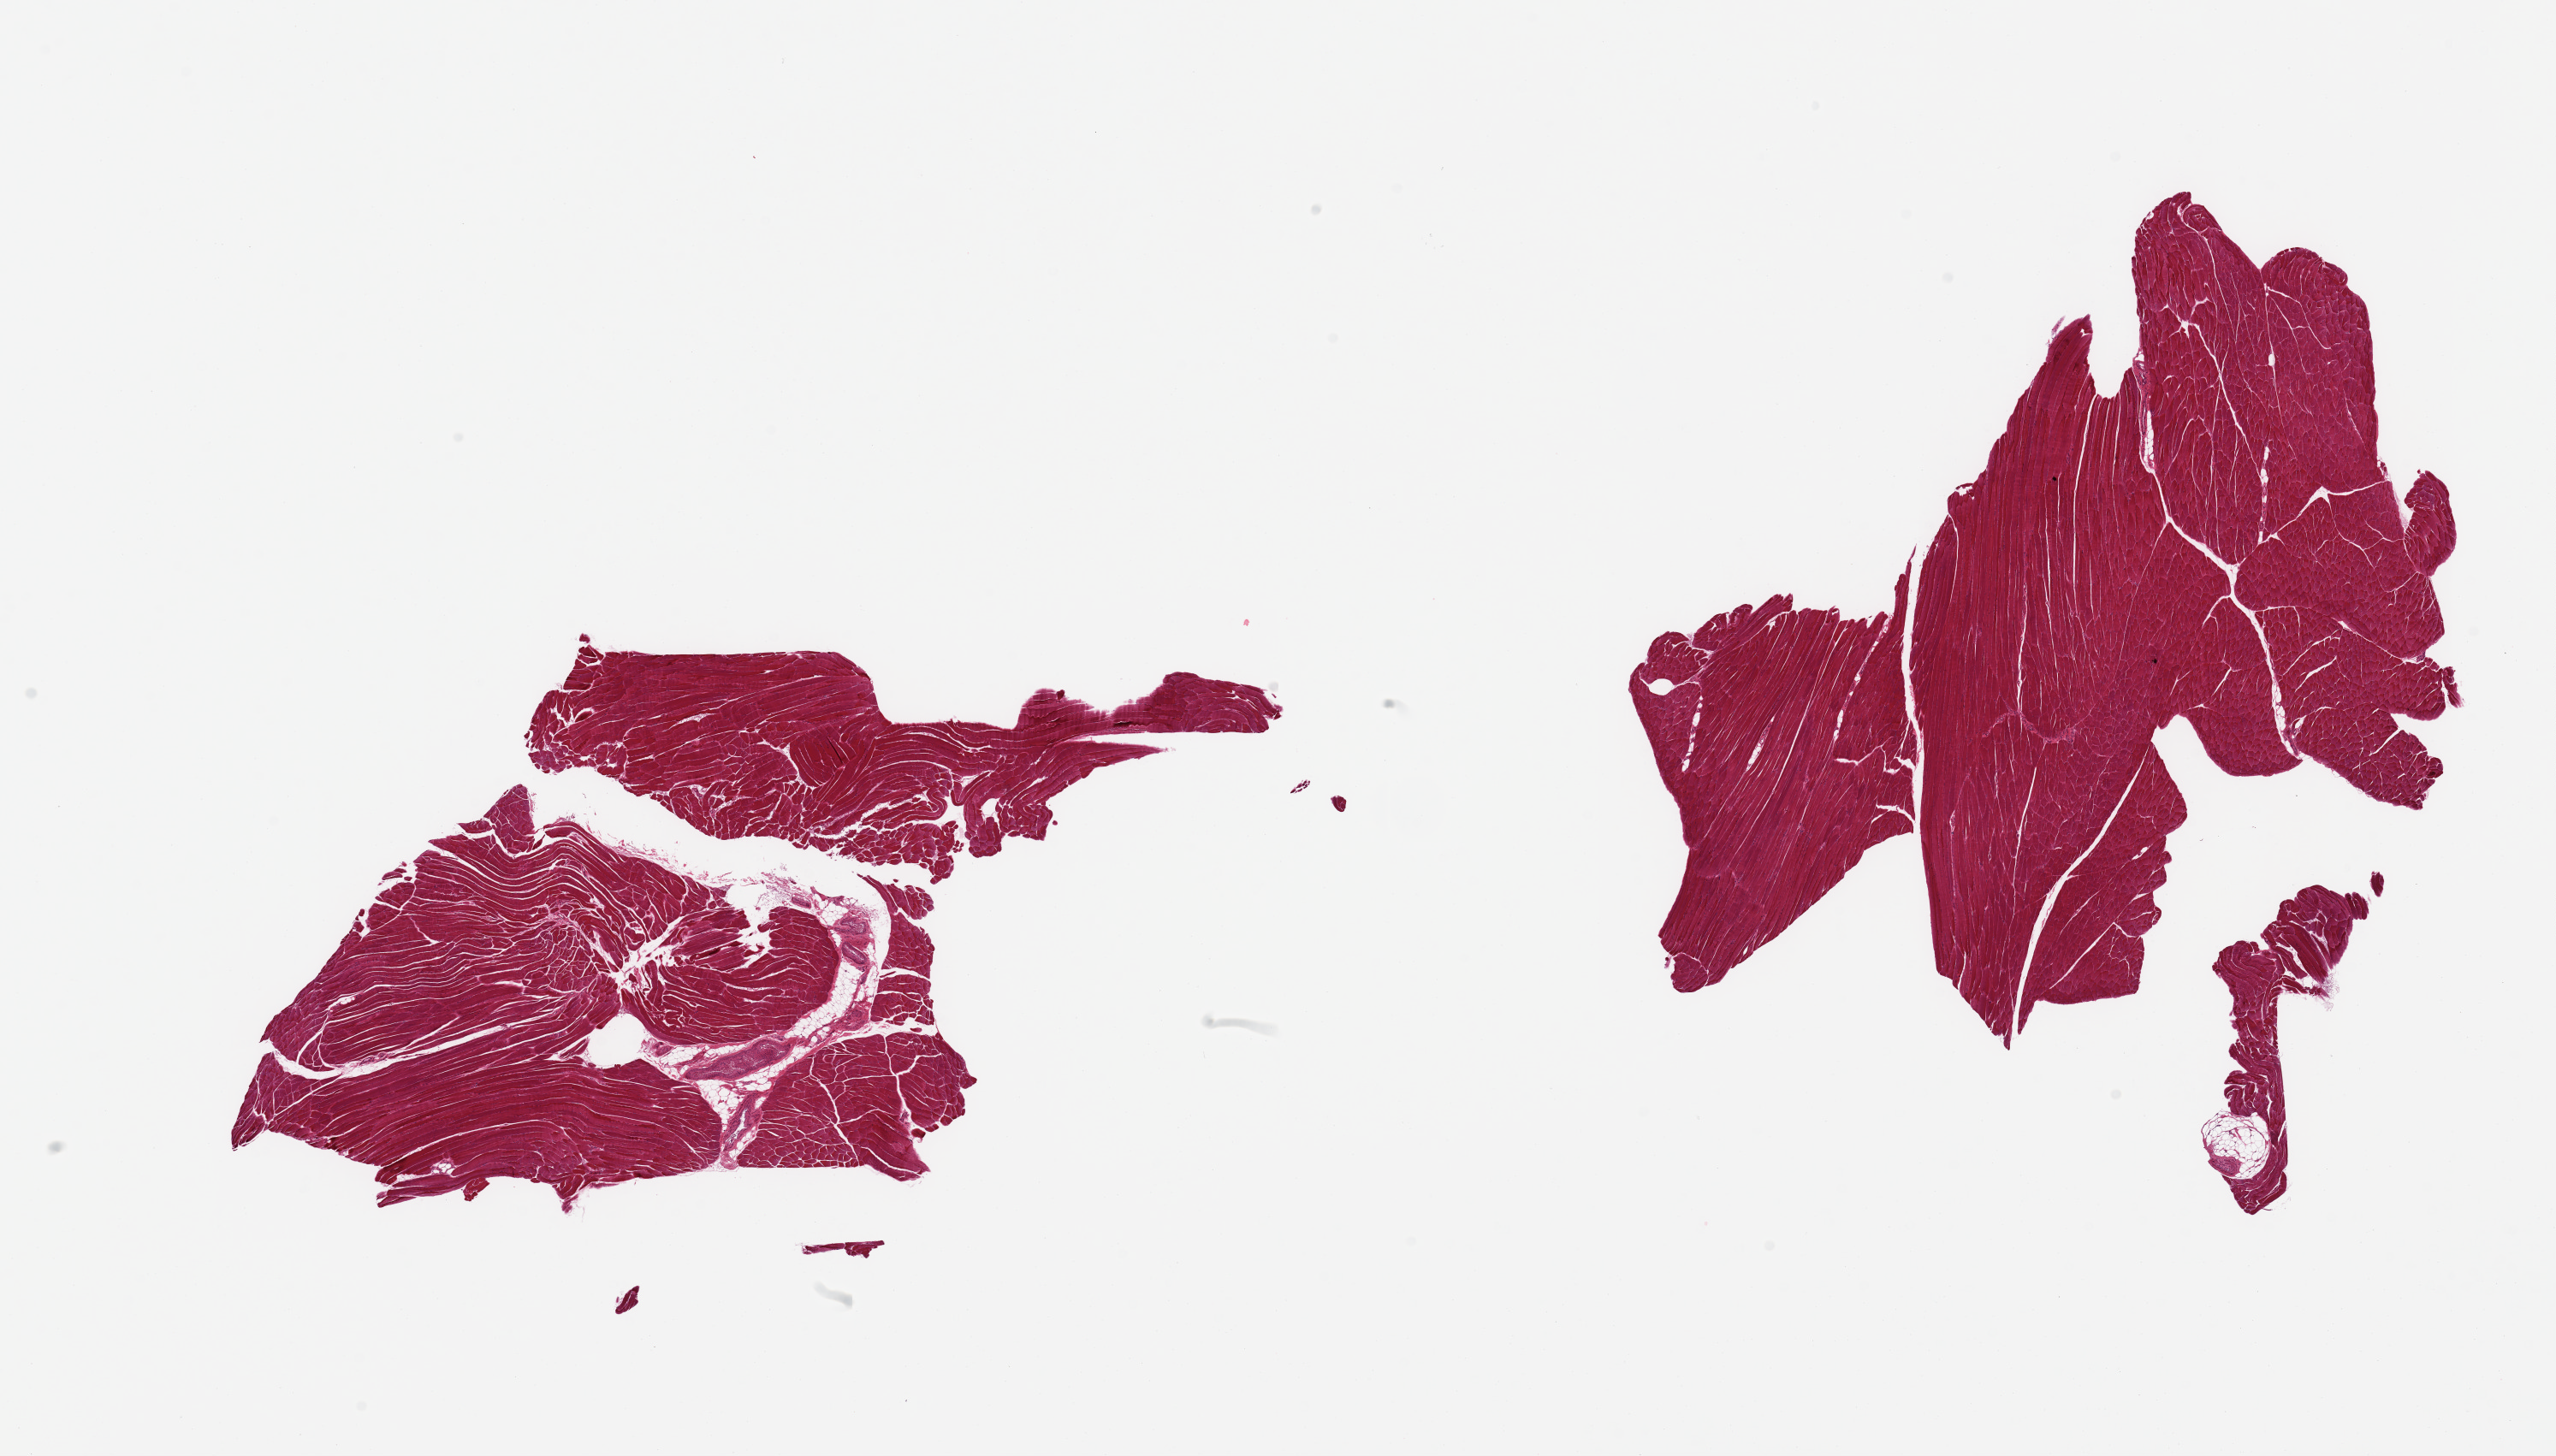
Hematoxylin and eosin (H&E) whole-slide image — whole scanned area (about 23.6 x 13.5 mm) shown as a low-resolution overview; PAXgene-fixed paraffin-embedded (PFPE) section; sampled site (target tissue): skeletal muscle; tissue donor sample. Female donor.
* pathologist's review note for this sample: 2 pieces; no fat content